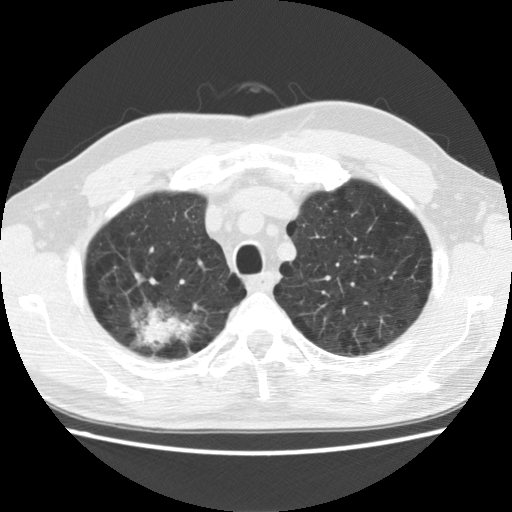
Low-dose screening chest CT, one axial slice. Slice 112 of 142 in the series (ordered by position). Reconstruction kernel STANDARD. 120 kVp. Lung window (W 1500 / L -600 HU). 512 × 512 image matrix, field of view 340 × 340 mm.
Outlined on this slice (expert manual segmentation):
- lesion 1 (tumor, upper lobe of right lung): box from (x=142, y=320) to (x=172, y=345) px